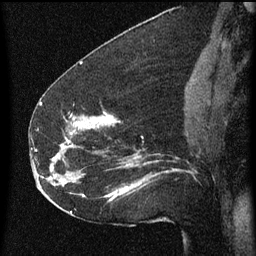
Breast MRI (dynamic contrast-enhanced), one sagittal slice; dynamic contrast-enhanced series, image 2 of 3 at this slice position (ordered by acquisition); 1.5 T; TE 4.2 ms, TR 8 ms; 2 mm slice thickness; 256 × 256 image matrix, field of view 180 × 180 mm. Patient: female, 52 years.
Outlined on this slice (semi-automatic segmentation, software-assisted and operator-edited):
- analysis volume of interest (the breast-tissue region the enhancement analysis was run in; not a lesion): box from (x=54, y=112) to (x=178, y=207) px
- tumour enhancement mask (voxels above the 70 % enhancement threshold inside the analysis volume of interest): (x=61, y=112)–(x=129, y=195)